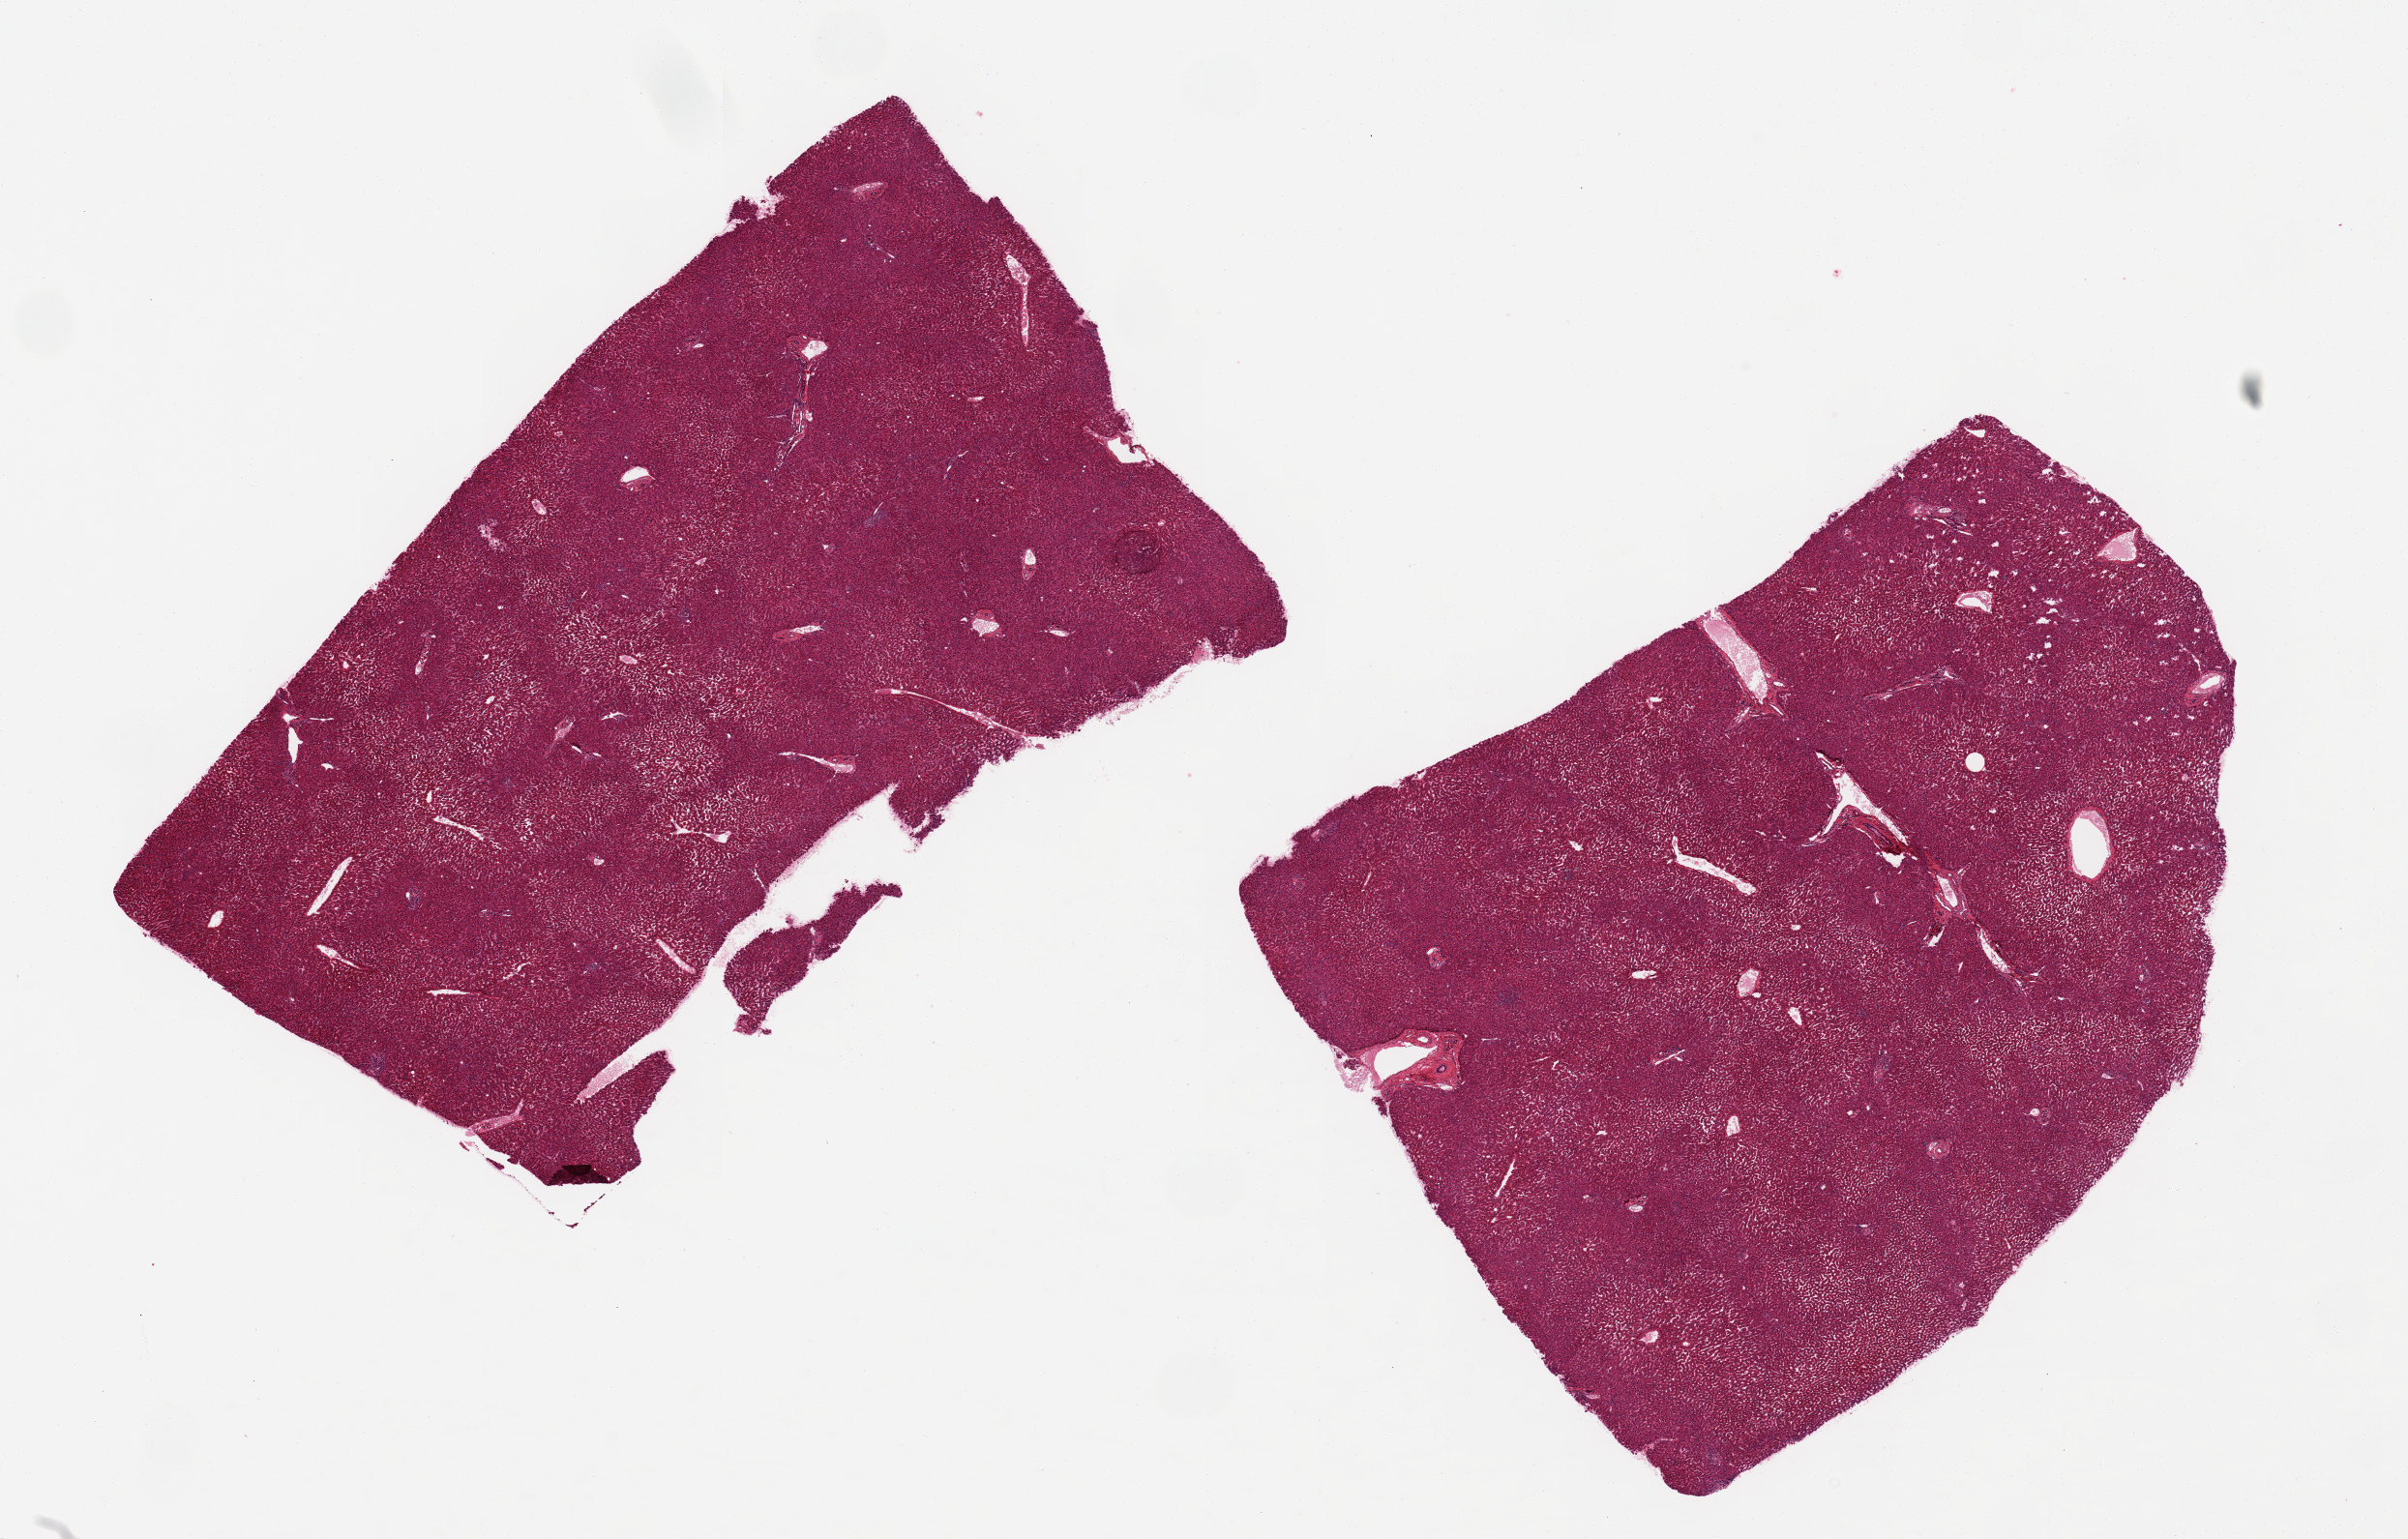
Digitized haematoxylin and eosin-stained section, brightfield, a low-resolution overview of the entire scanned area, about 19.7 x 12.6 mm (acquisition: 20x scan); PAXgene-fixed, paraffin-embedded tissue; section of liver (target tissue); donor tissue sample. Female donor.
Pathologist's review note for this sample: 2 pieces,~ 6x8 mm; central sinusoidal dilatation; focal fragmentation.